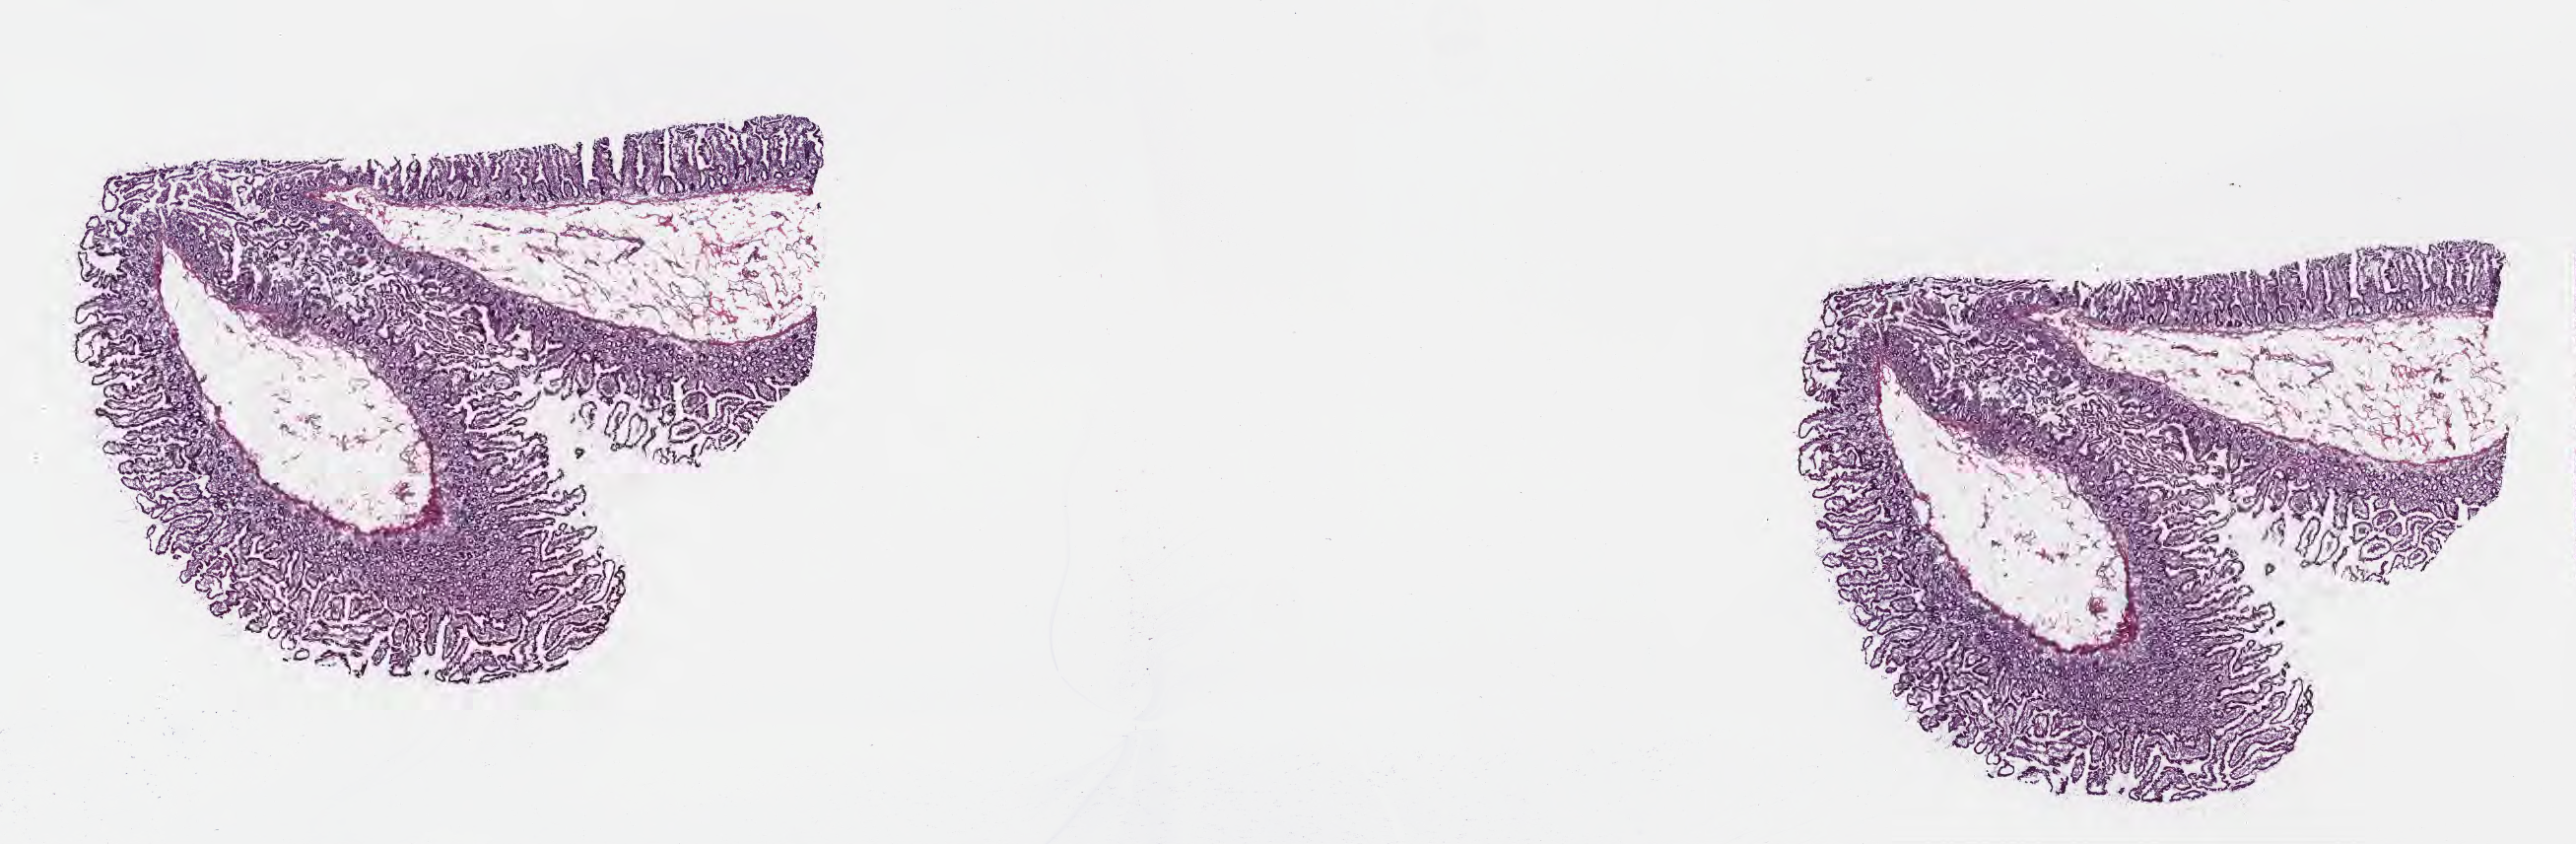
Digitized H&E-stained section — low-resolution overview of the scanned area, about 21.1 x 6.9 mm. Cryosection. Non-tumor (normal tissue) sample from a patient with infiltrating duct carcinoma, NOS. Anatomic site: head of pancreas. Patient: male, age at initial diagnosis 57 years. Slide review estimates, as recorded: tumor cells 0%, tumor nuclei 0%, stromal cells 30%, necrosis 0%, normal cells 70%. Infiltration values recorded for this section: lymphocyte infiltration 44%, monocyte infiltration 1%, neutrophil infiltration 0%.
This section: non-tumor tissue sample; the patient's diagnosis is given above.